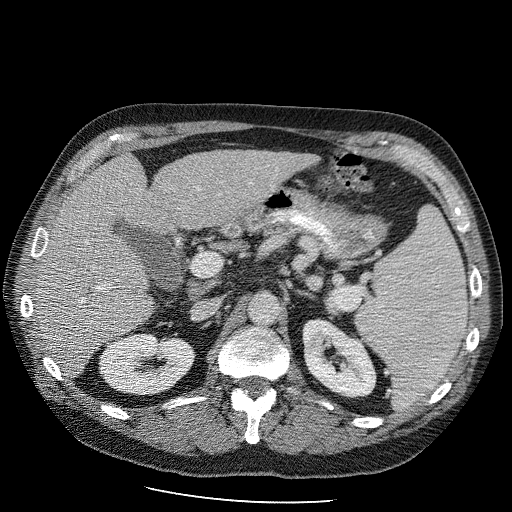
Contrast-enhanced abdominal CT (liver protocol), one axial slice; slice 50 of 98 in the series (ordered by position); reconstruction kernel STANDARD; 120 kVp; soft-tissue window (W 400 / L 40 HU); 2.5 mm slice thickness; 512 × 512 image matrix, field of view 400 × 400 mm. Case-level facts recorded for this patient, not image findings: diagnosis: hepatocellular carcinoma (patient treated with transarterial chemoembolisation; whether this scan precedes or follows treatment is not stated here); TNM stage (as recorded): Stage-II; Child-Pugh class: B.
Outlined on this slice (semi-automatically segmented with operator editing):
- liver parenchyma outside the tumour (the mass and vessels are separate outlines, so this box may not span the whole liver): box from (x=28, y=148) to (x=321, y=376) px
- liver vessels: (x=38, y=181)–(x=252, y=288)